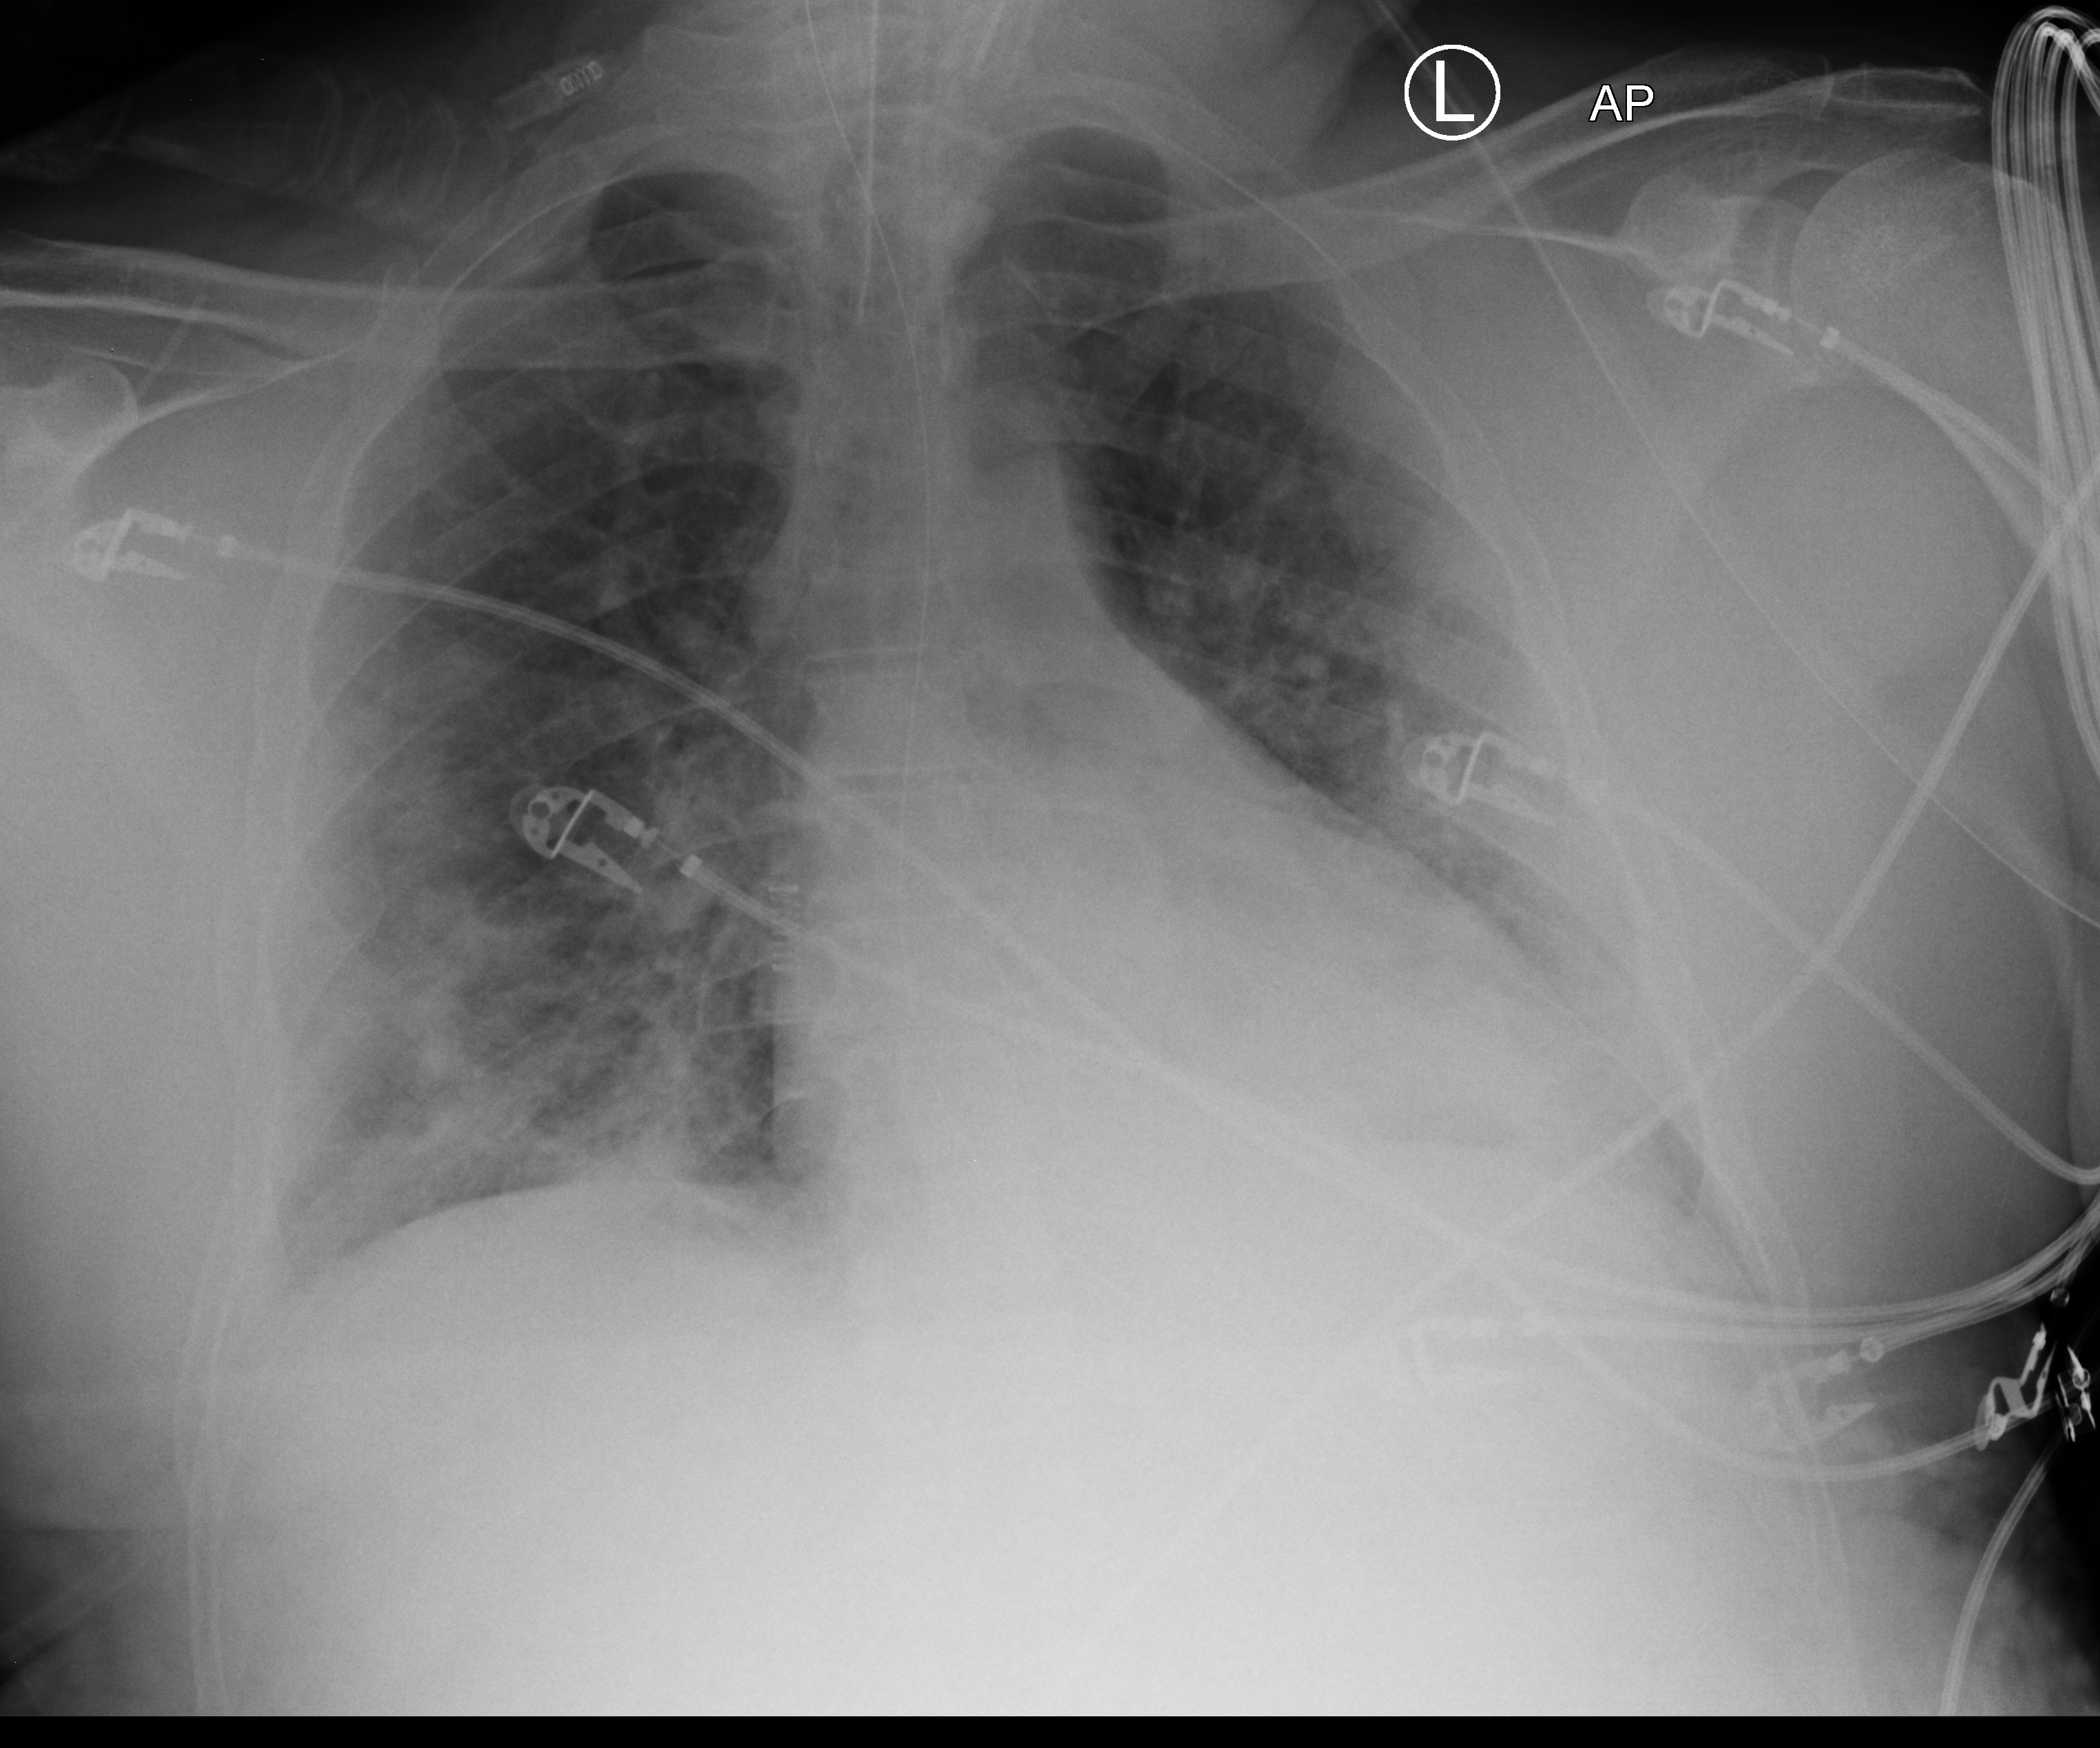
Chest X-ray (portable), anteroposterior (AP) projection. Male patient hospitalised with COVID-19, age 18–59 years.
From the hospital-stay record, not from the radiograph (when in the stay this image was taken is not recorded): admitted to intensive care during this hospital stay: yes.